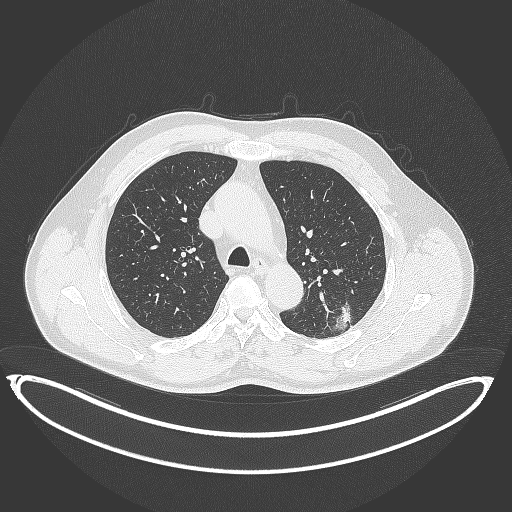
Chest CT, one axial slice. Position 254 of 399 along the scan axis. Reconstruction kernel B70f. 120 kVp. Lung window (W 1500 / L -600 HU). 512 × 512 image matrix, field of view 469 × 469 mm. Patient: male, 58 years. Case-level facts recorded for this patient, not image findings: clinical TNM (as recorded): T1c N0 M0; histopathological grade: G1-2.
Annotated regions visible in this slice (rectangle marked by the reading radiologist):
- lung tumour (recorded histology: adenocarcinoma): bounding box (x1, y1, x2, y2) in pixels: (332, 298, 358, 332)